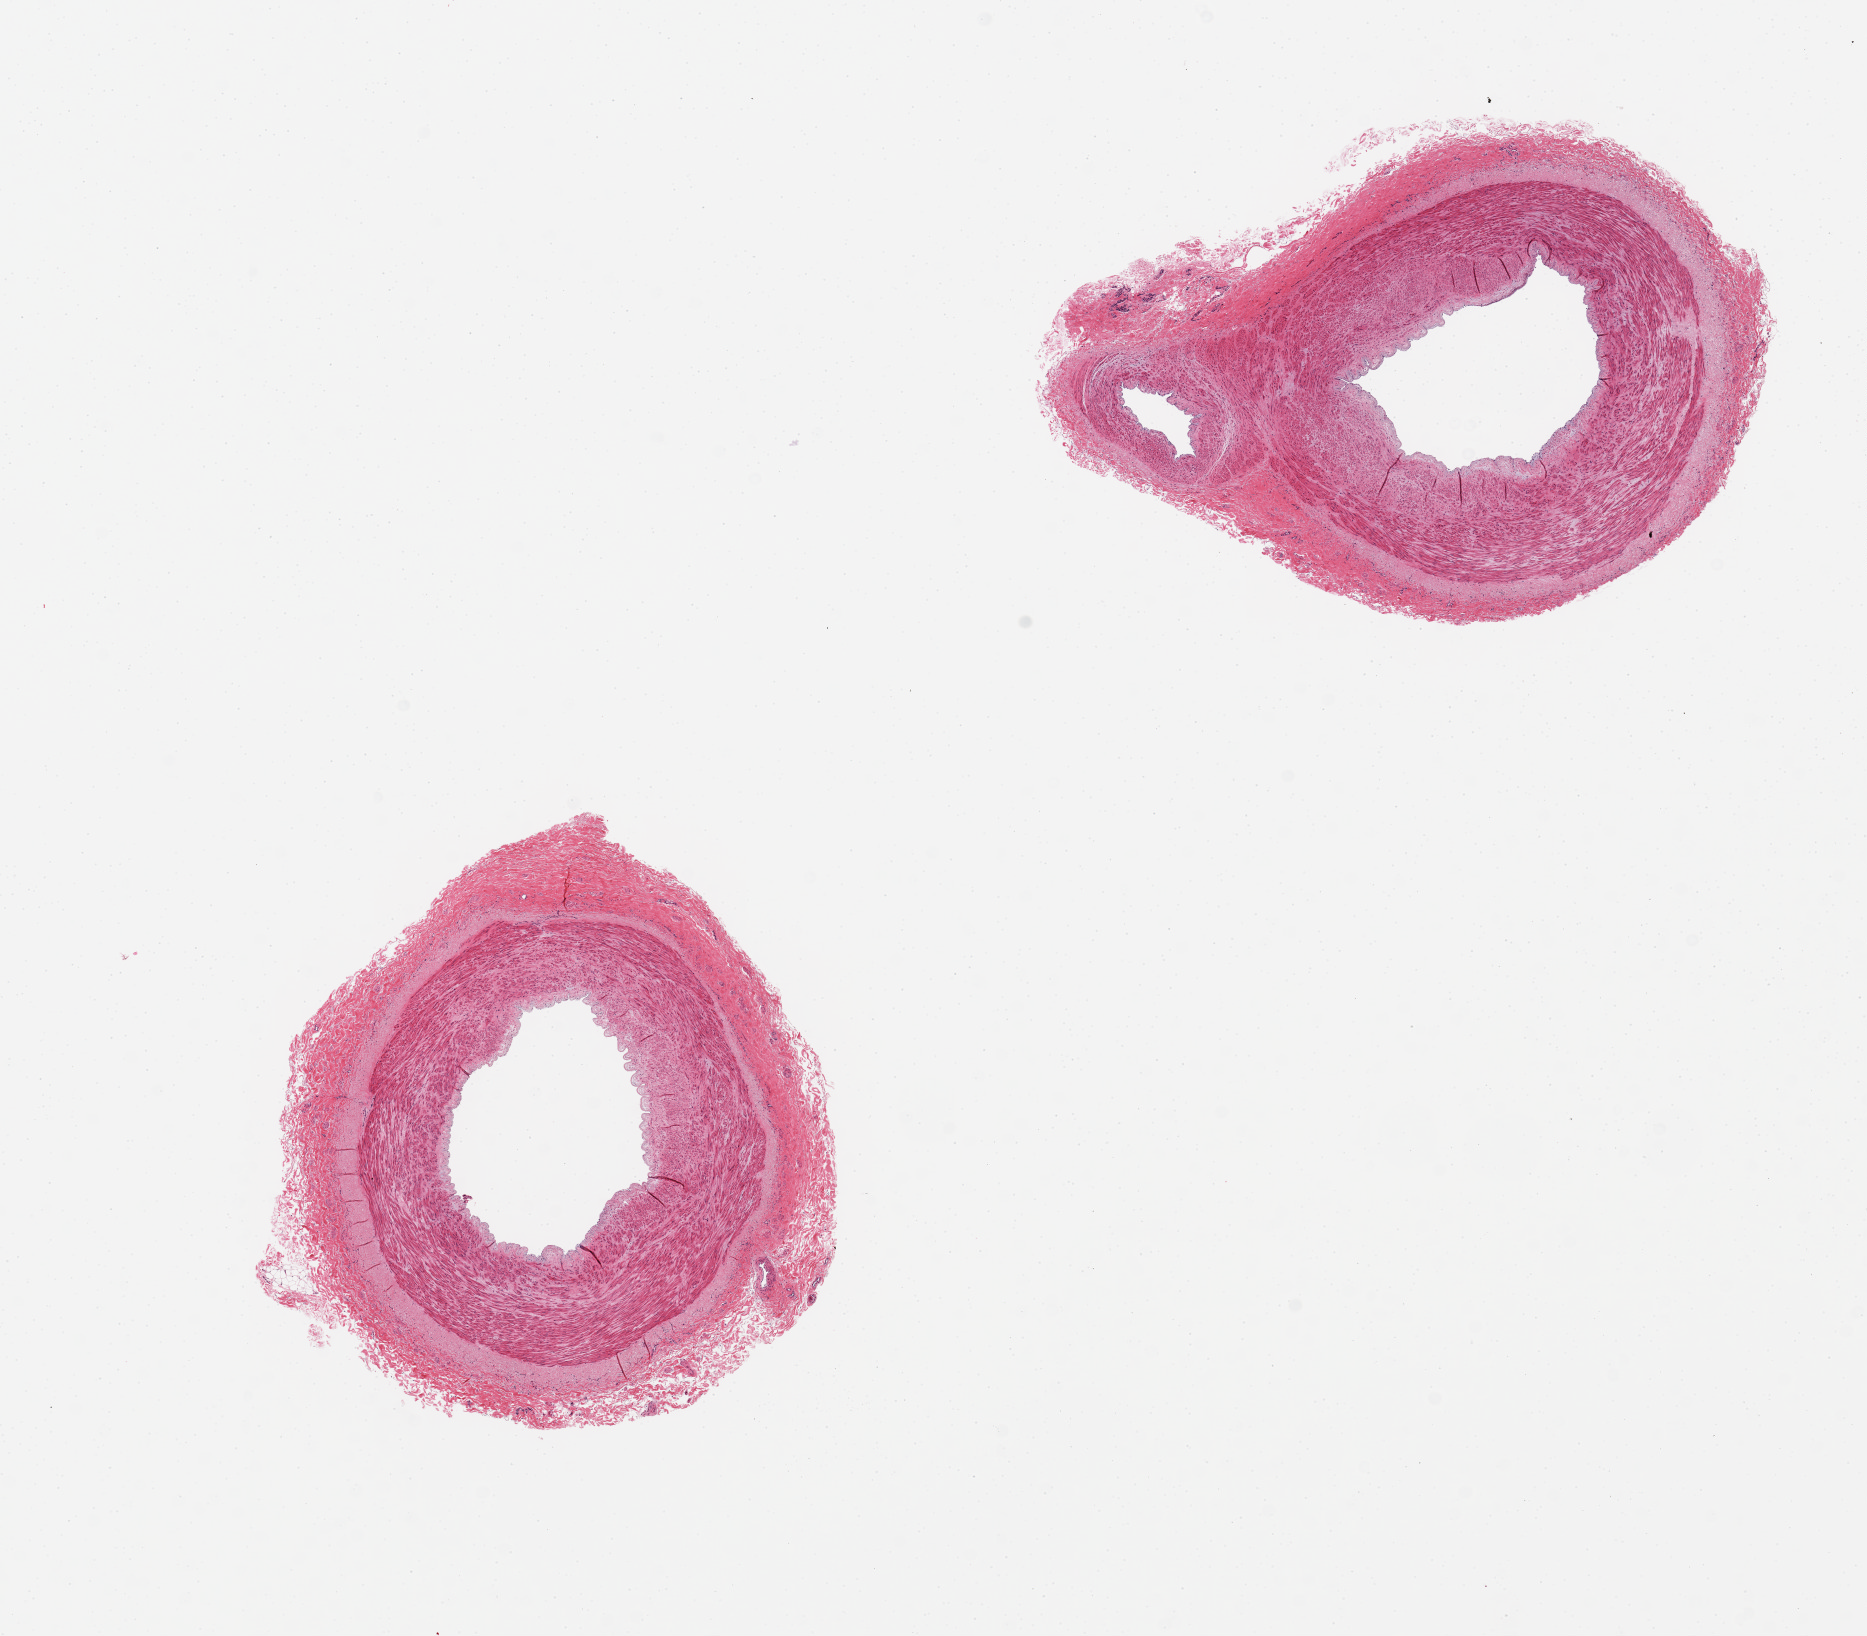
Whole-slide image, H&E stain — whole scanned area (about 14.8 x 12.9 mm) shown as a low-resolution overview; PAXgene-fixed, paraffin-embedded tissue; sampled site (target tissue): tibial artery; donor tissue sample. Donor: female.
Review note (as recorded): 2 pieces, well trimmed.